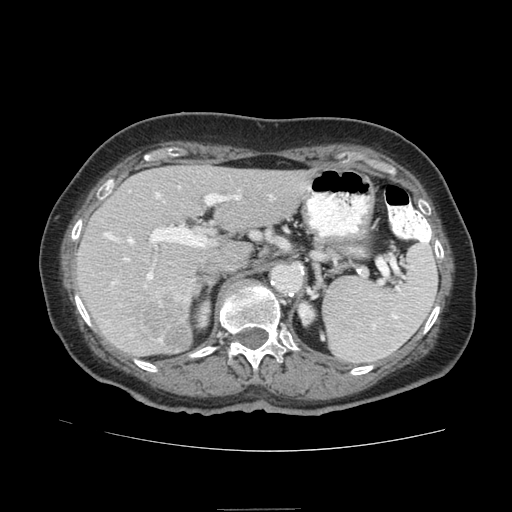
Contrast-enhanced abdominal CT (liver protocol), one axial slice. Position 48 of 95 along the scan axis. Reconstruction kernel STANDARD. 140 kVp. Soft-tissue window (W 400 / L 40 HU). 2.5 mm slice thickness. 512 × 512 image matrix, field of view 360 × 360 mm. From the clinical record (not read from this slice): diagnosis: hepatocellular carcinoma (patient treated with transarterial chemoembolisation; whether this scan precedes or follows treatment is not stated here); TNM stage (as recorded): Stage-IVA; Child-Pugh class: B; tumour nodularity: uninodular.
Annotated regions visible in this slice (semi-automatic segmentation, software-assisted and operator-edited):
- liver parenchyma outside the tumour (the mass and vessels are separate outlines, so this box may not span the whole liver): bounding box <76,166,314,356> (left, top, right, bottom; pixels)
- mass: <136,289,192,351>
- liver vessels: <104,186,309,285>